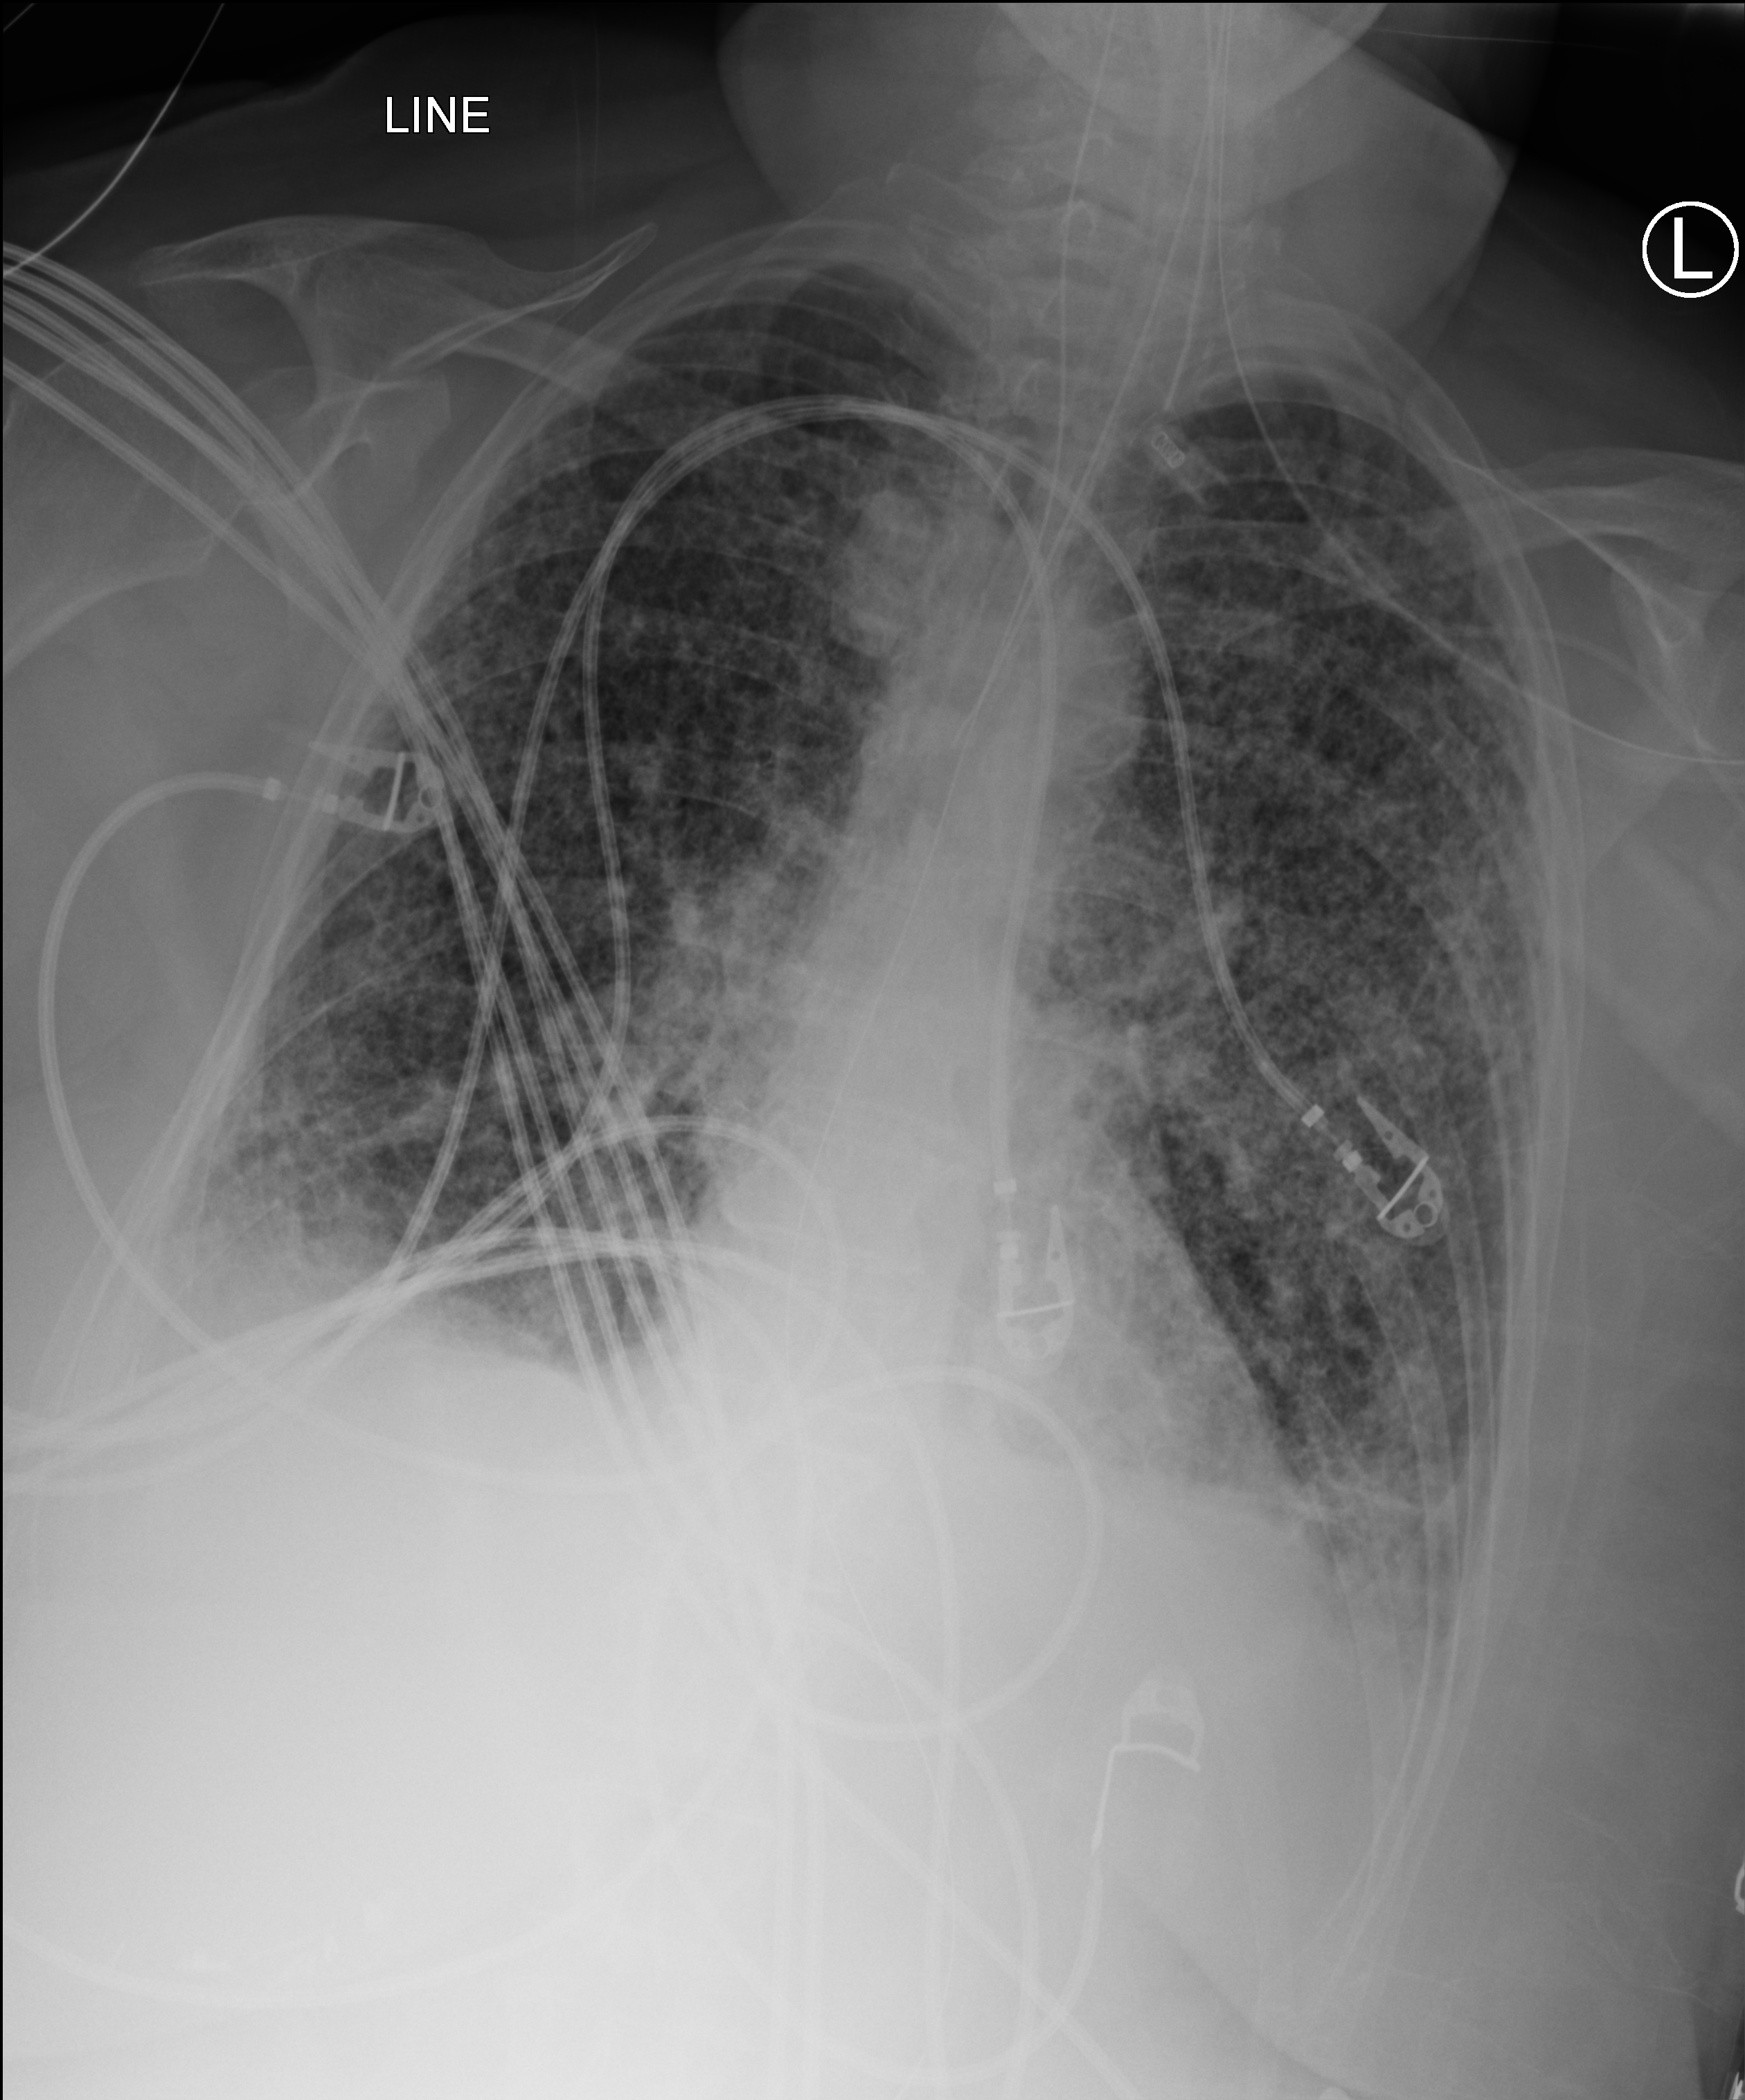
Portable chest radiograph. Patient hospitalised with COVID-19; female, aged 60–74 years.
From the hospital-stay record, not from the radiograph (when in the stay this image was taken is not recorded): length of hospital stay: 19 days.